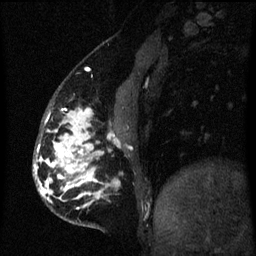
Breast MRI (dynamic contrast-enhanced), one sagittal slice; position 19 of 60 along the scan axis; dynamic contrast-enhanced series, image 2 of 3 at this slice position (ordered by acquisition); 1.5 T; TE 4.2 ms, TR 8 ms; 2 mm slice thickness; 256 × 256 image matrix, field of view 190 × 190 mm. Female patient, age 50 years.
Annotated regions visible in this slice (semi-automatically segmented with operator editing):
- analysis volume of interest (the breast-tissue region the enhancement analysis was run in; not a lesion): bounding box [x1, y1, x2, y2] px = [34, 109, 118, 226]
- tumour enhancement mask (voxels above the 70 % enhancement threshold inside the analysis volume of interest): [34, 109, 110, 209]